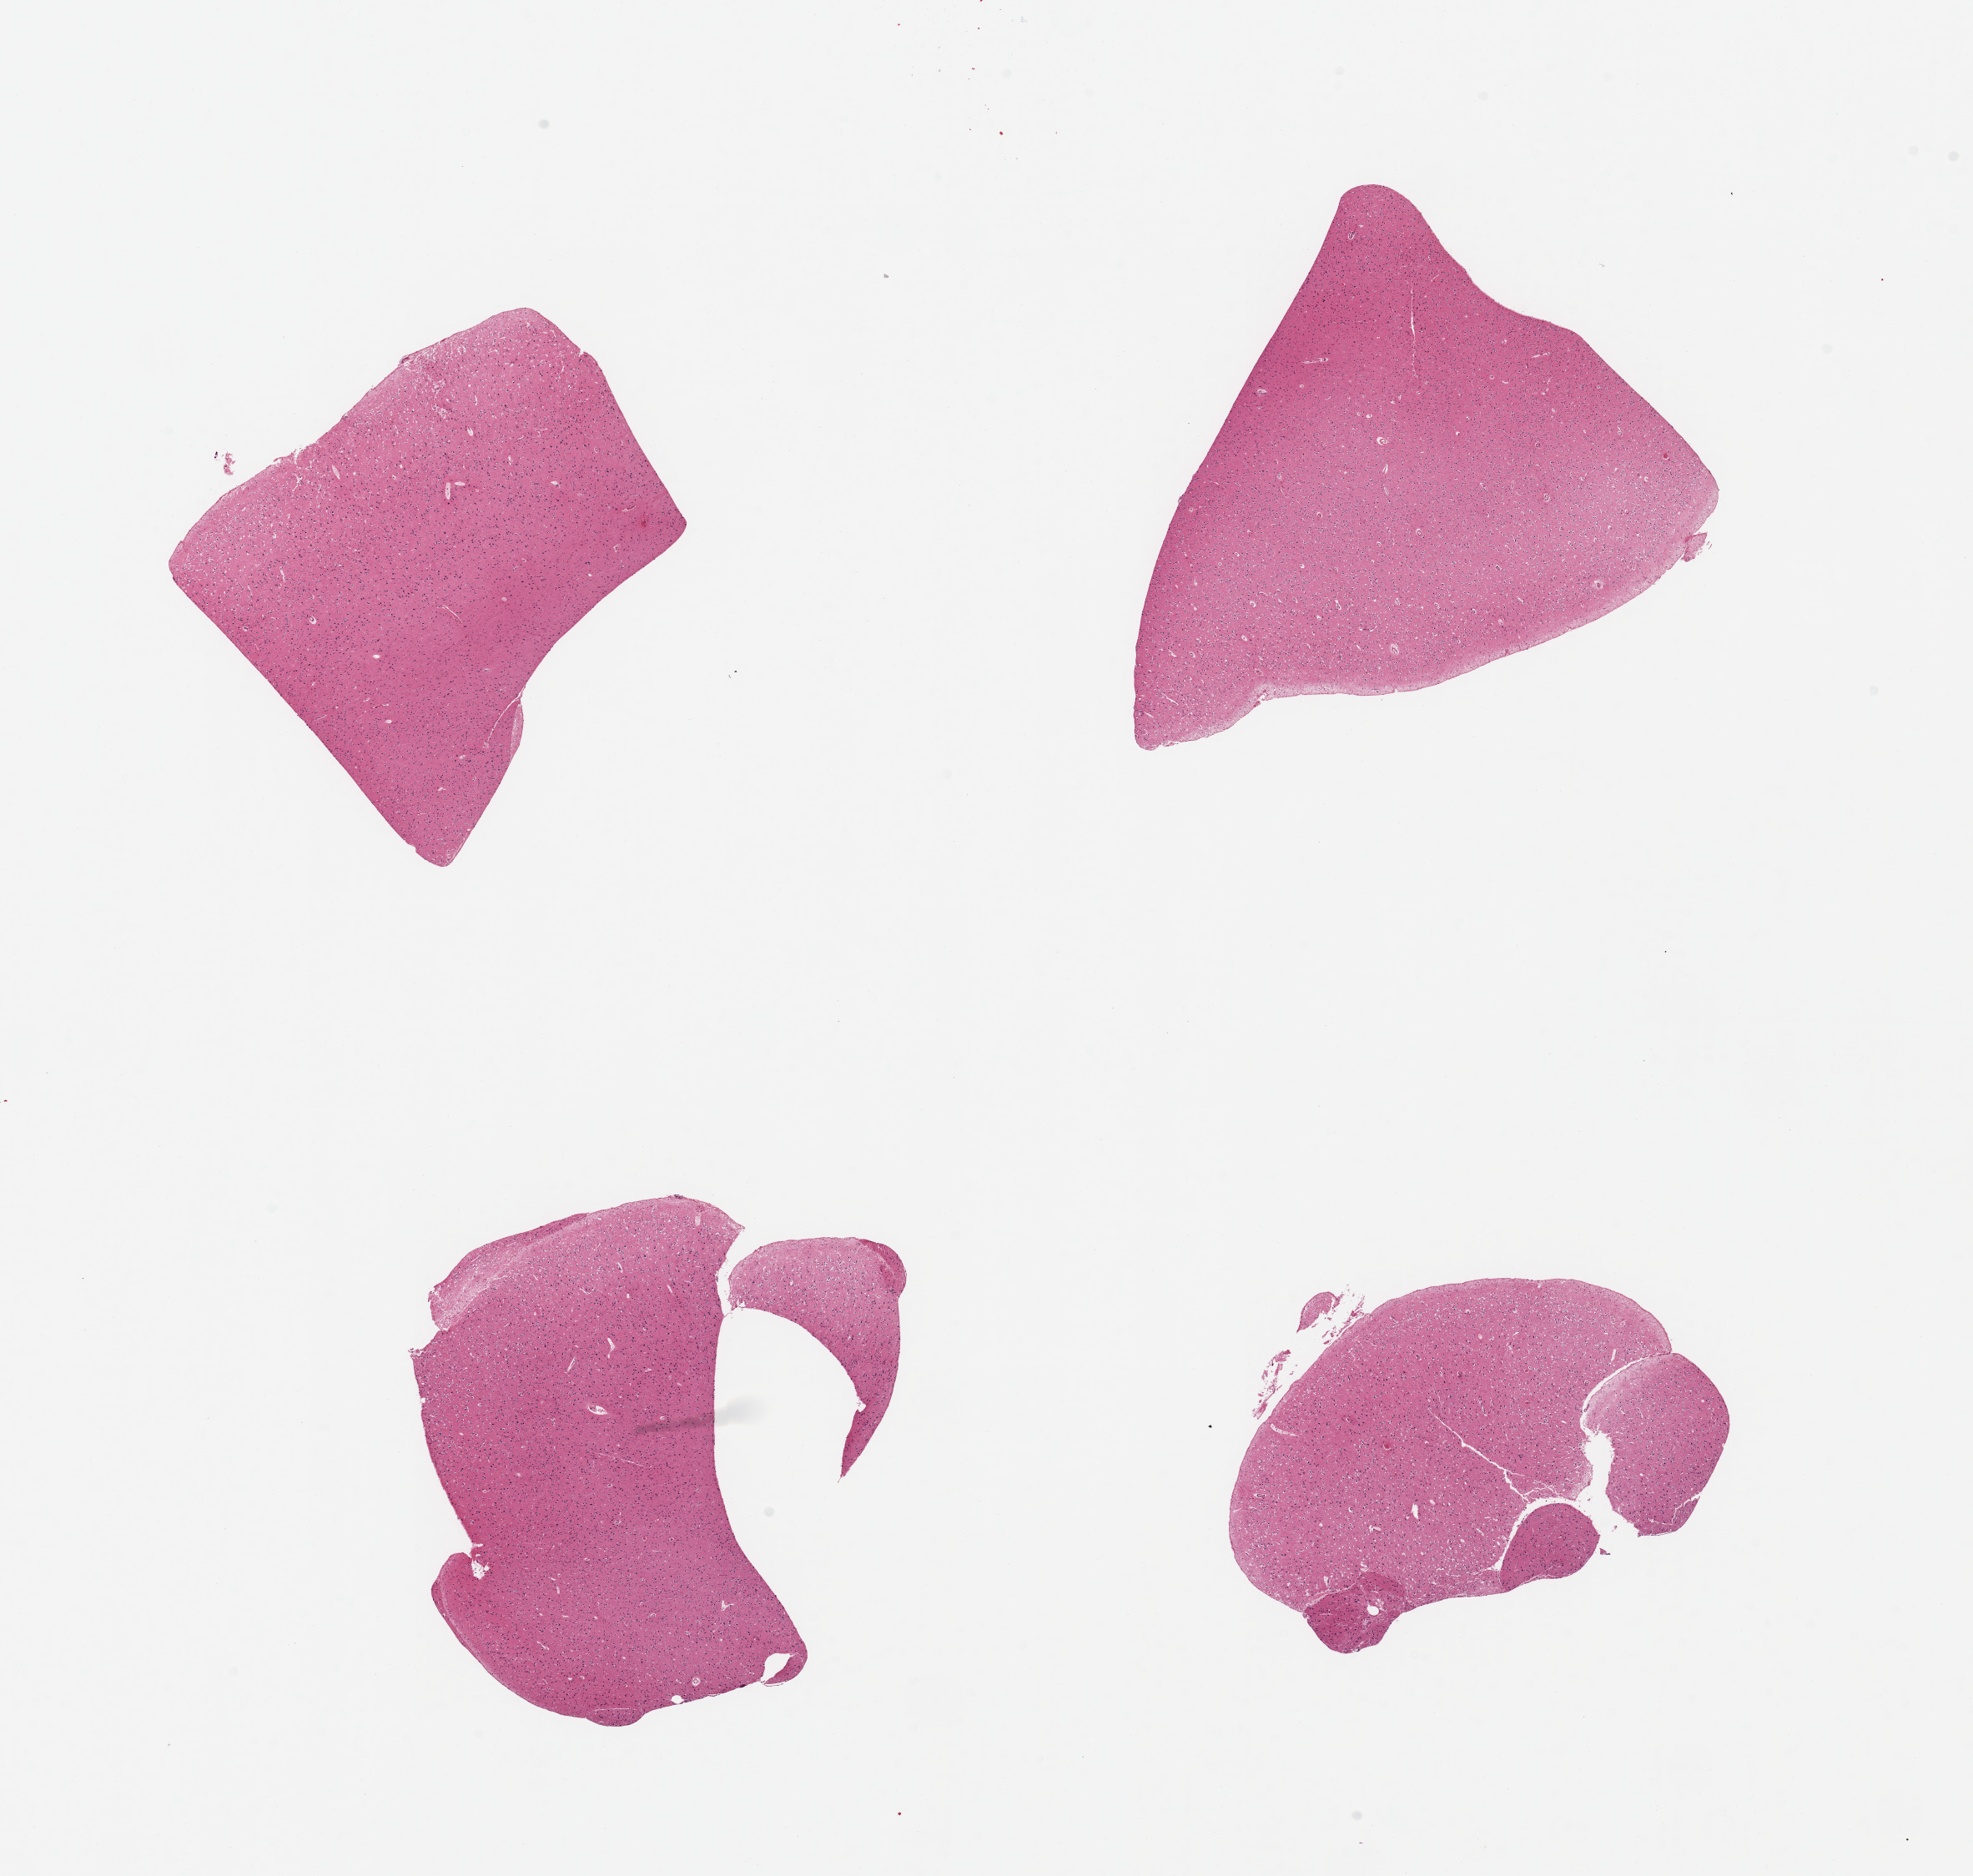
Whole-slide image, H&E stain, brightfield — a low-resolution overview of the entire scanned area, about 18.7 x 17.8 mm, PAXgene-fixed paraffin-embedded (PFPE) section, sampled site (target tissue): cerebral cortex, tissue donor sample. Female donor.
Review note (as recorded): 4 pieces, no abnormalities.